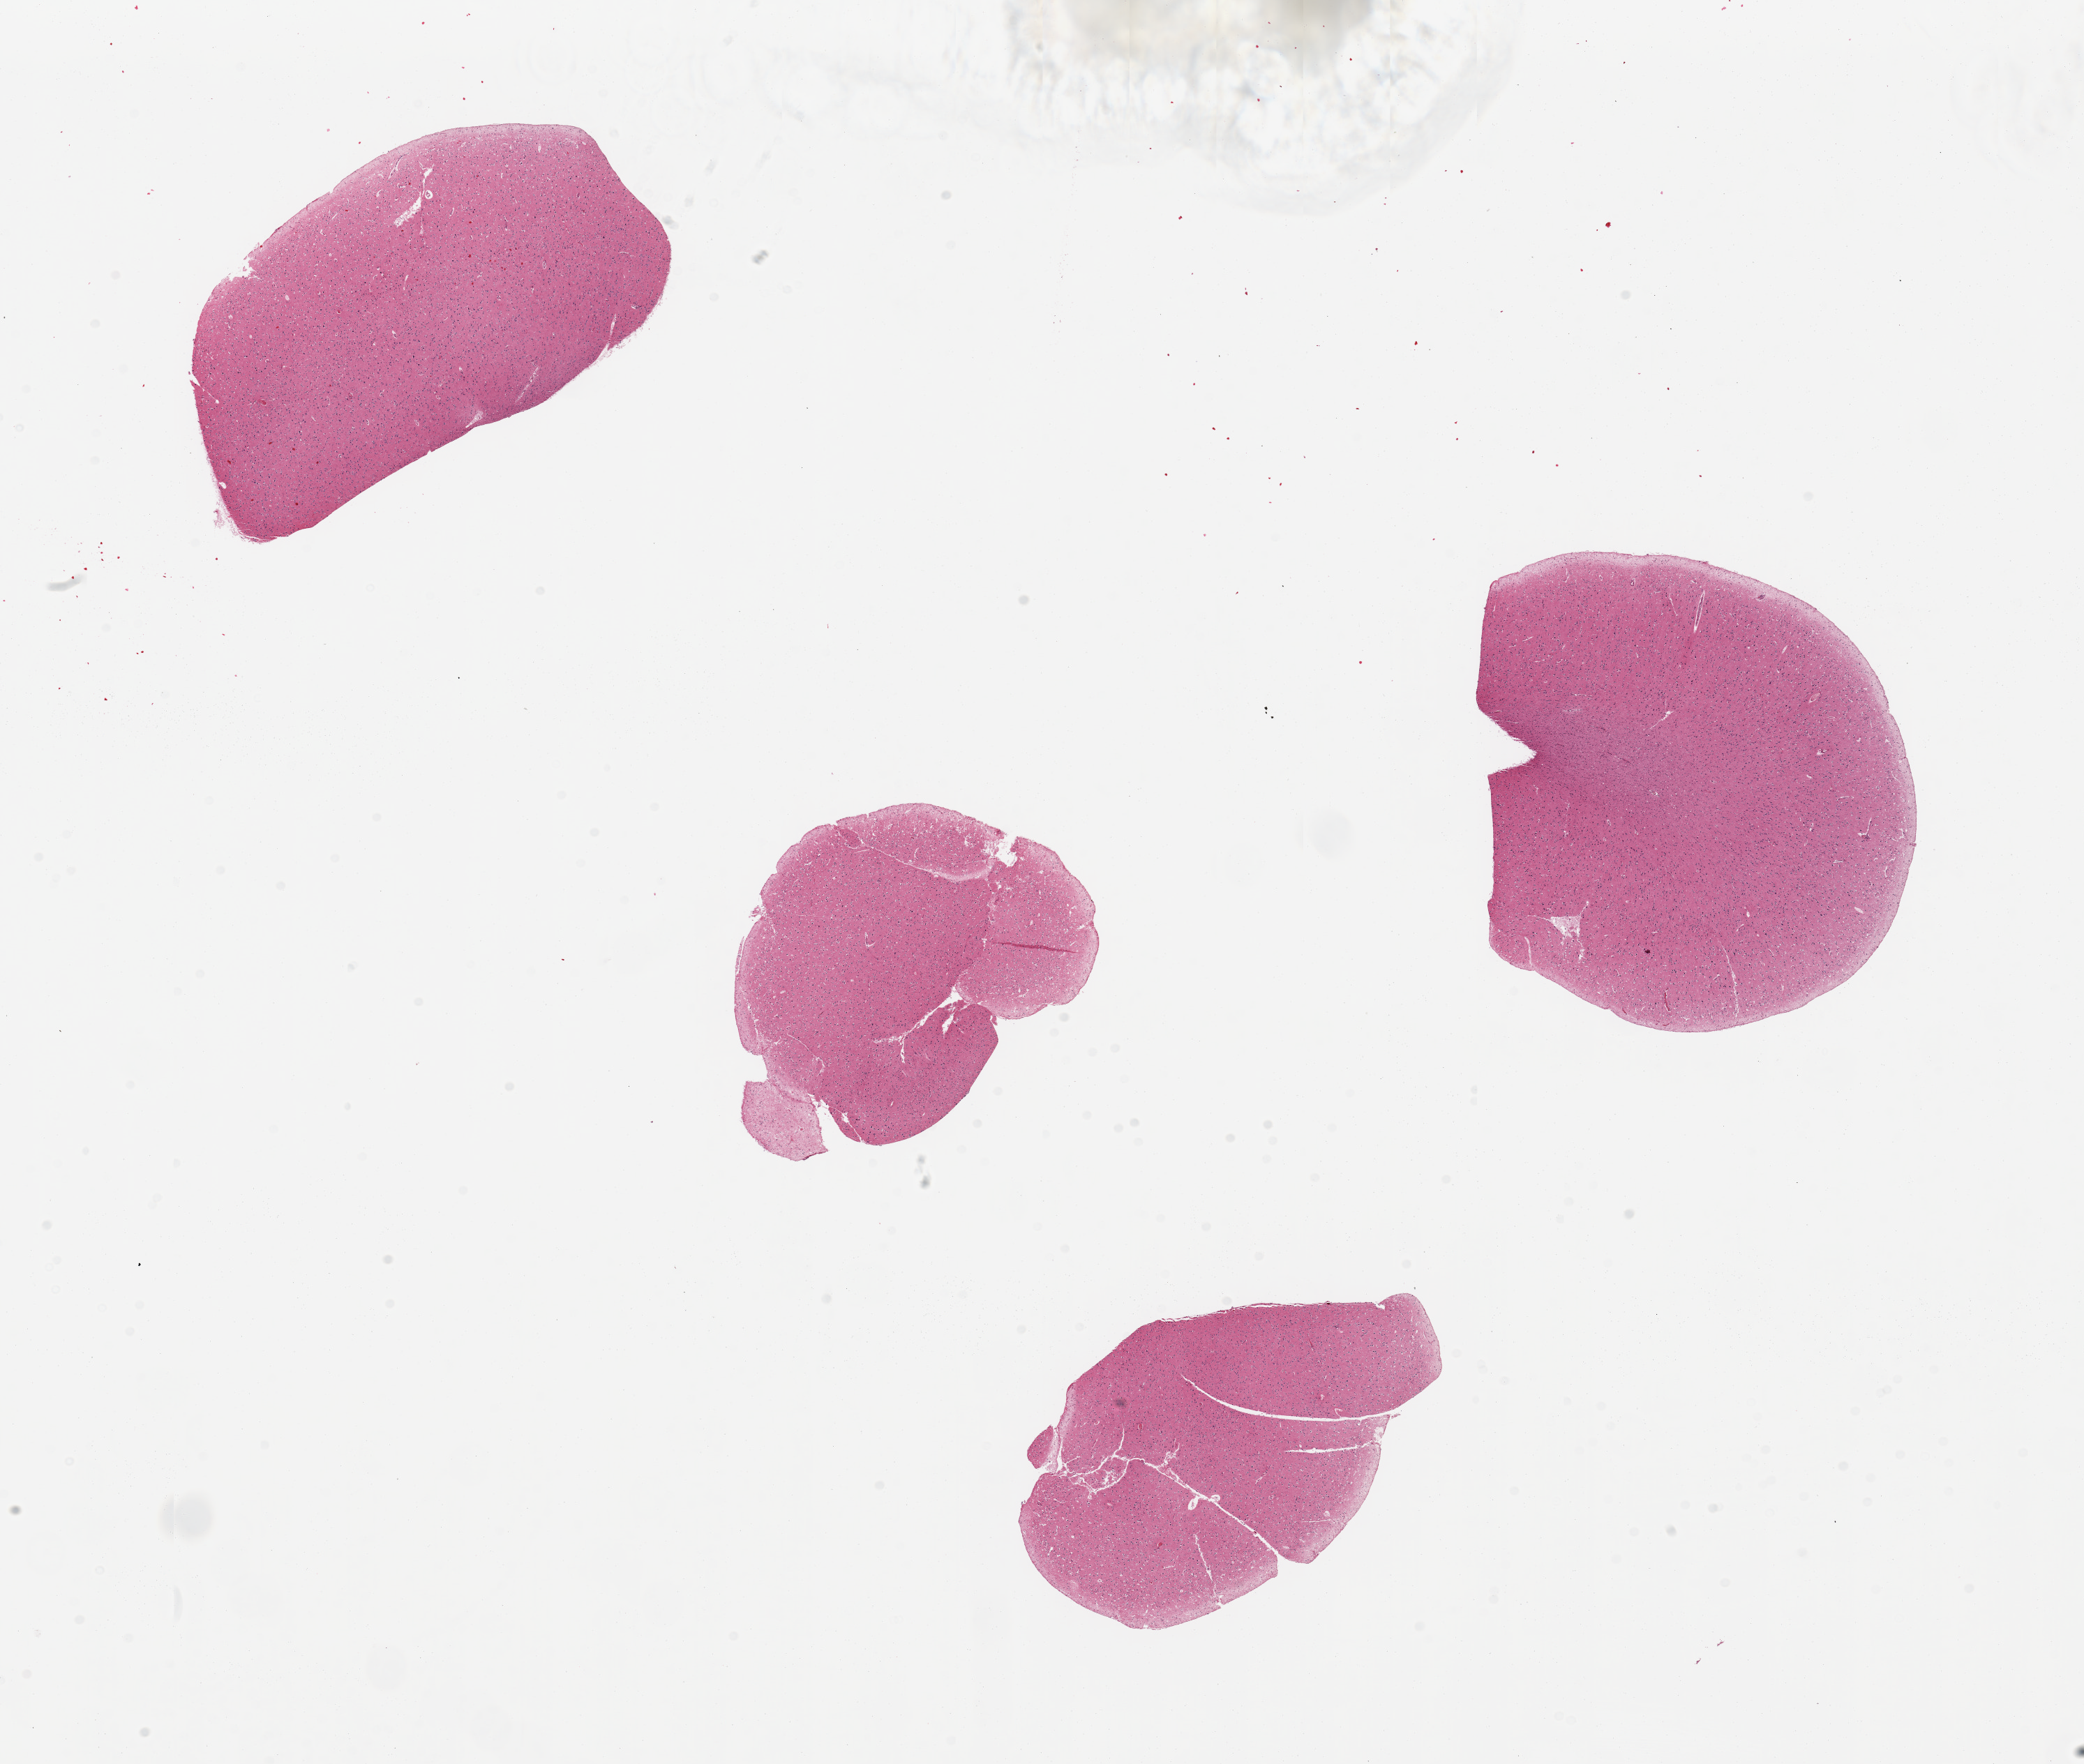
H&E whole-slide image — whole scanned area (about 23.6 x 20.0 mm, acquisition: 20x scan) shown as a low-resolution overview. PAXgene-fixed paraffin-embedded (PFPE) section. Target tissue: cerebral cortex. Tissue donor sample.
Review note (as recorded): 4 pieces, no abnormalities.